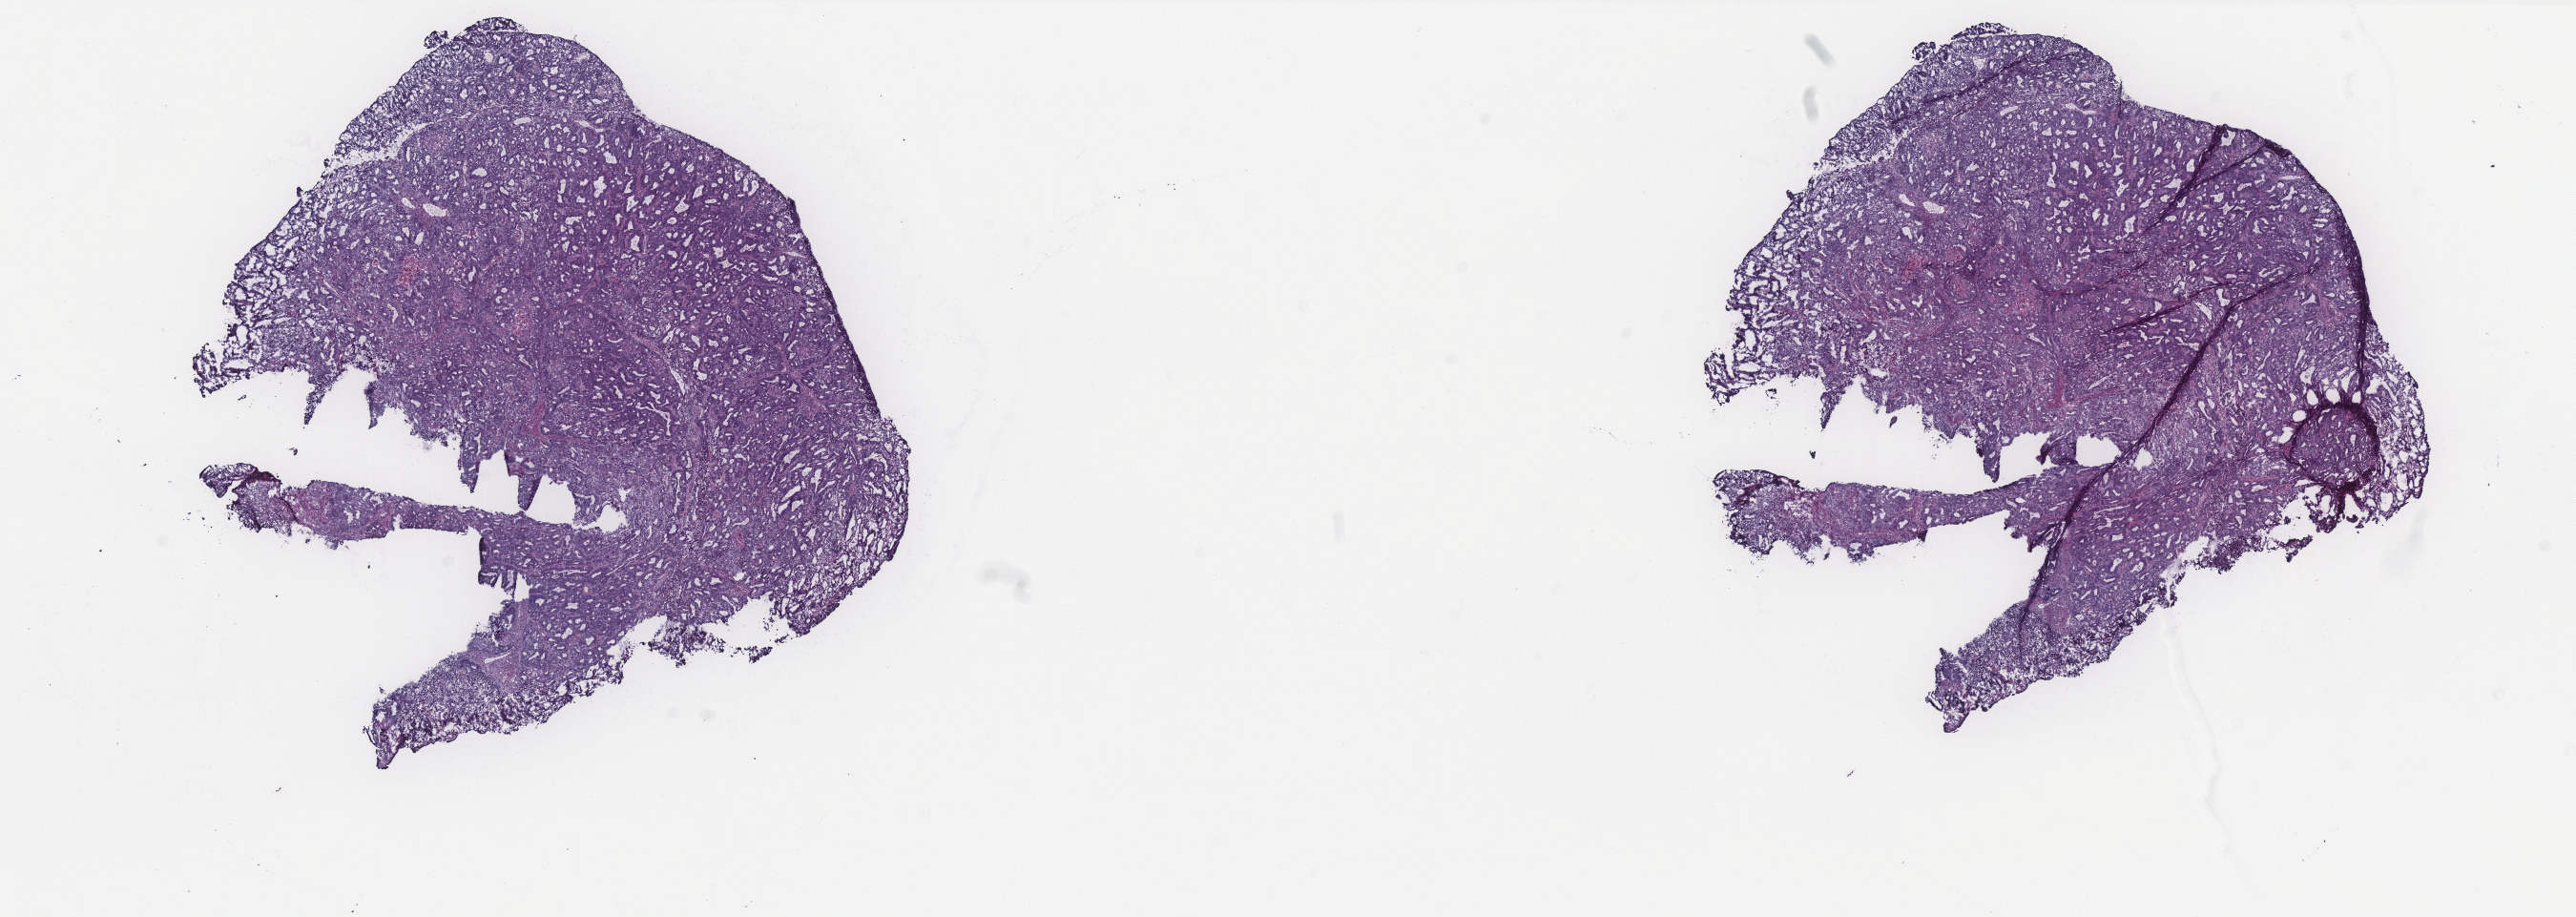
Digitized H&E-stained tissue section (whole slide), low-resolution overview of the scanned area, about 21.6 x 7.7 mm; frozen section from the top of the tissue portion; sample: primary tumour, uterus. Female patient; age at initial diagnosis 51 years. Histologic grade: G1 (well differentiated). Pathologist review of this section (percent, as recorded): tumour cells 100%, tumour nuclei 80%, normal cells 0%, stromal cells 0%, necrosis 0%. Infiltration values recorded for this section: lymphocyte infiltration 0%, monocyte infiltration 0%, neutrophil infiltration 0%.
FIGO stage: IA. Lymph nodes positive (case pathology): 0 of 20 examined. Pathologic diagnosis: Endometrioid adenocarcinoma, NOS (endometrium).